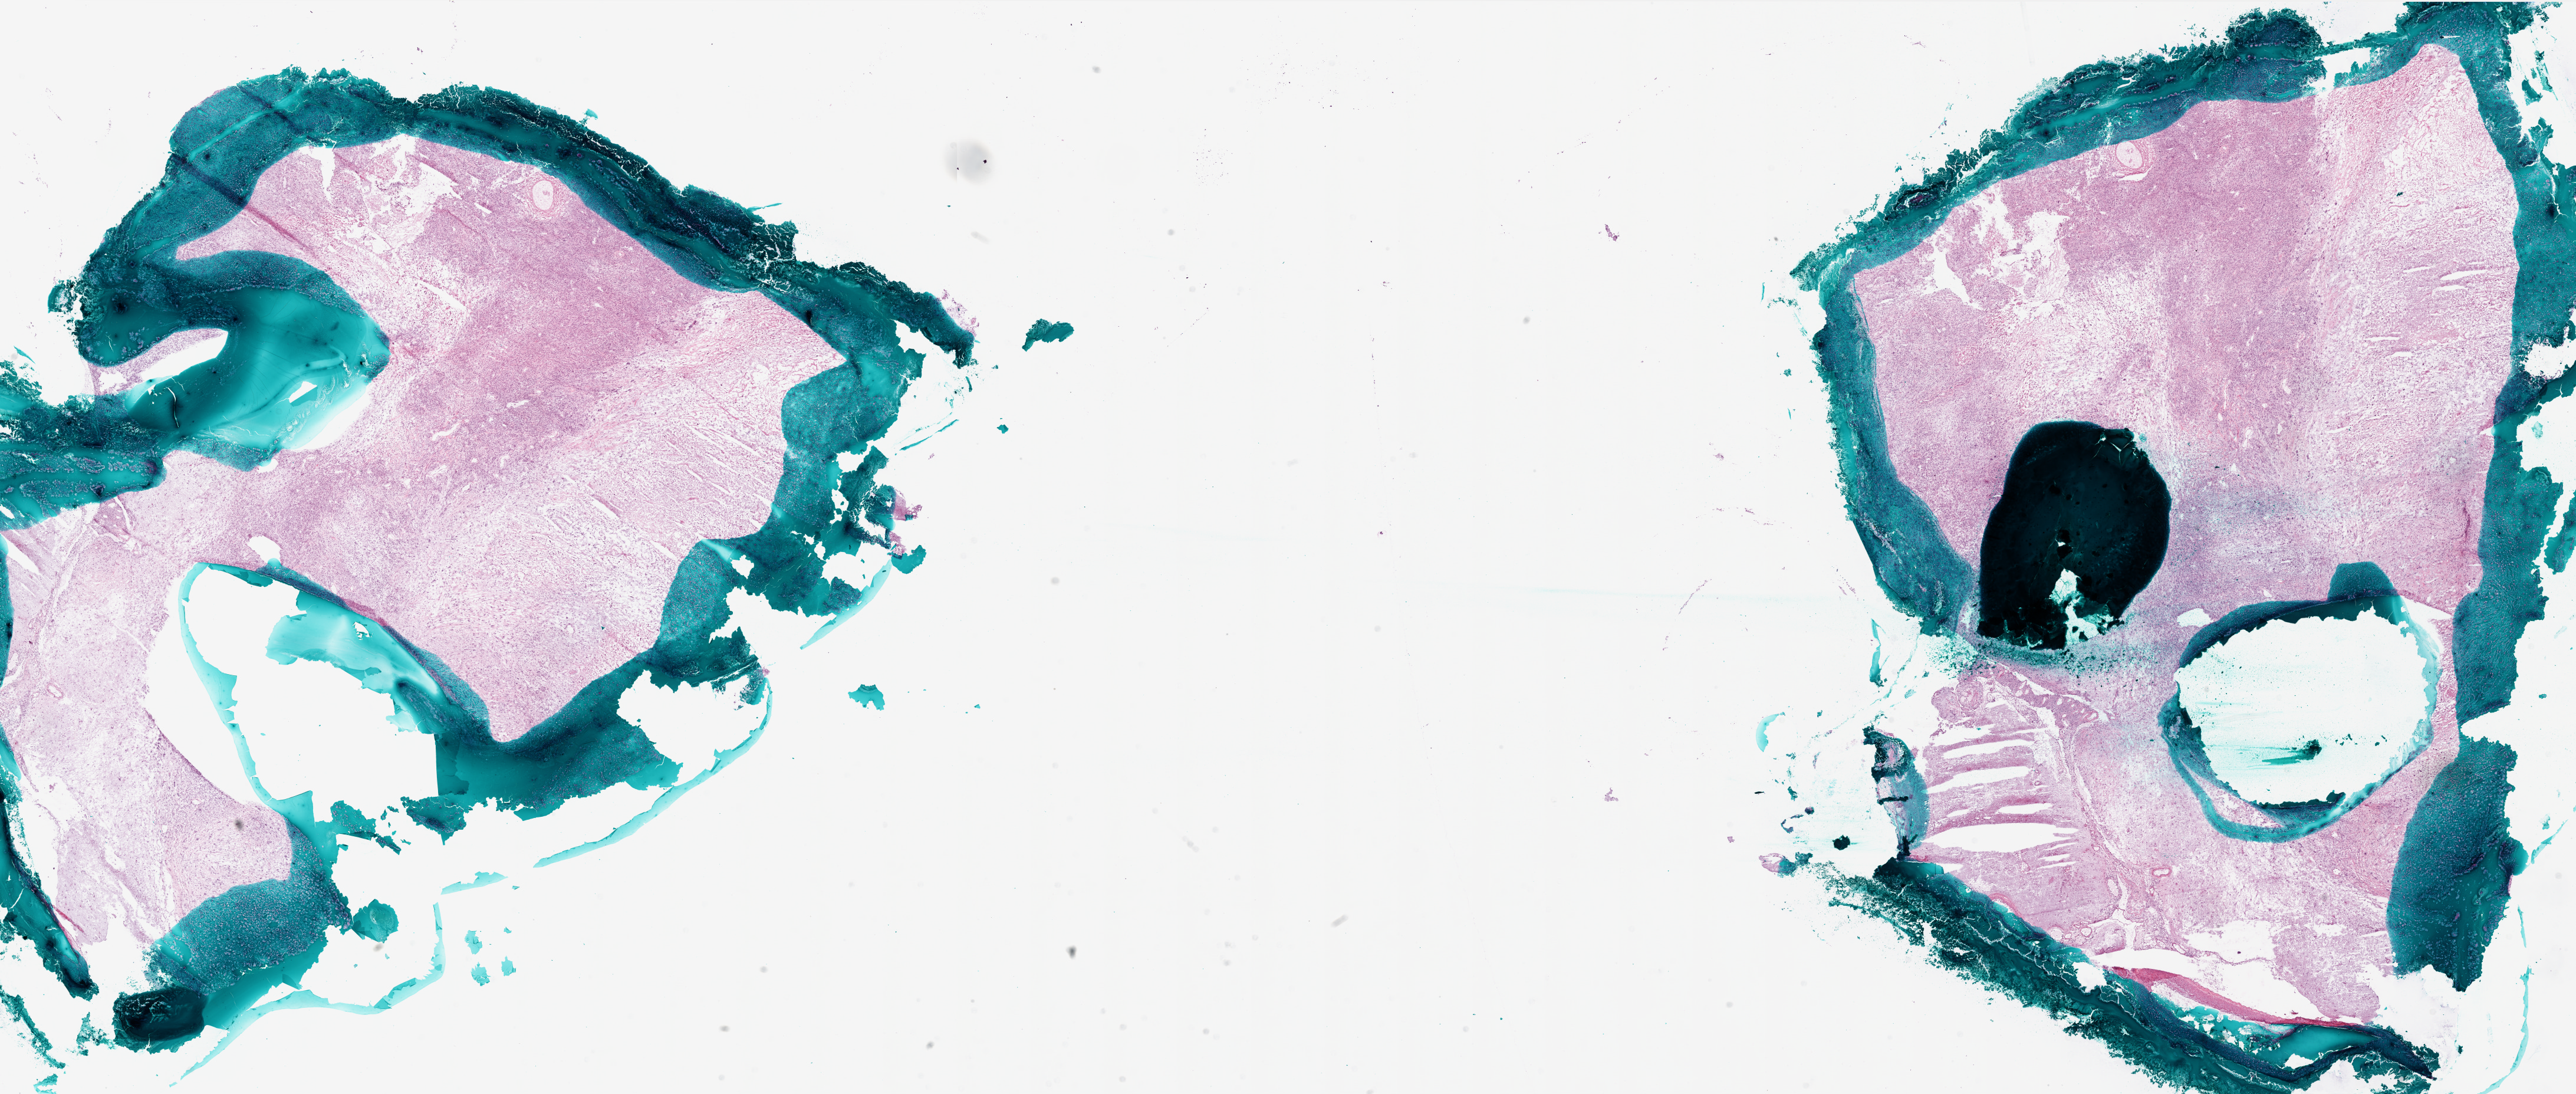
Digitized Hematoxylin and eosin (H&E) stained tissue section (whole slide), shown as a low-resolution overview of the whole scanned area (about 35.0 x 14.8 mm). Frozen section. Brain, primary tumour sample. Female, age 62 years at initial diagnosis. Slide review estimates, as recorded: tumour cells 60%, tumour nuclei 95%, normal cells 0%, stromal cells 20%, necrosis 20%.
* pathologic diagnosis: Glioblastoma